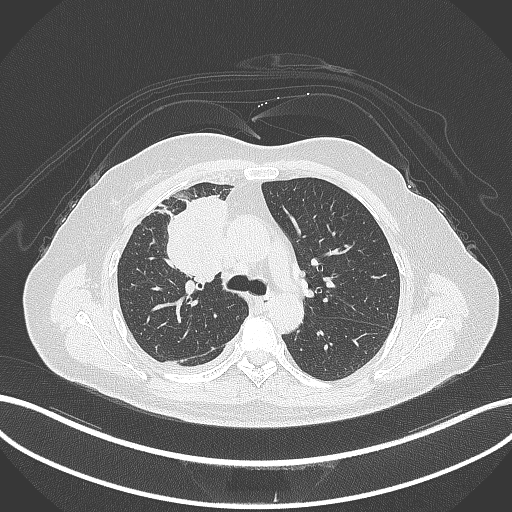
Chest CT, one axial slice. Slice 187 of 305 in the series (ordered by position). Lung window (W 1500 / L -600 HU). 1 mm slice thickness. 512 × 512 image matrix, field of view 400 × 400 mm. Female patient, age 52 years. Case-level facts recorded for this patient, not image findings: clinical TNM (as recorded): T3 N1 M1.
Outlined on this slice (bounding box drawn by a radiologist):
- lung tumour (recorded histology: adenocarcinoma): bounding box (x1, y1, x2, y2) in pixels: (163, 190, 230, 287)